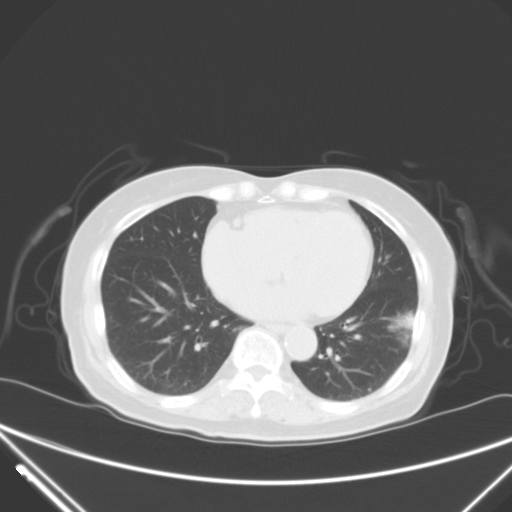
Chest CT, one axial slice; position 23 of 62 along the scan axis; lung window (W 1500 / L -600 HU); 512 × 512 image matrix. Female patient, age 82 years. Case-level facts recorded for this patient, not image findings: clinical TNM (as recorded): T1c N0 M0.
Structures marked on this image (rectangle marked by the reading radiologist):
- lung tumour (recorded histology: adenocarcinoma): bounding box <385,309,428,348> (left, top, right, bottom; pixels)